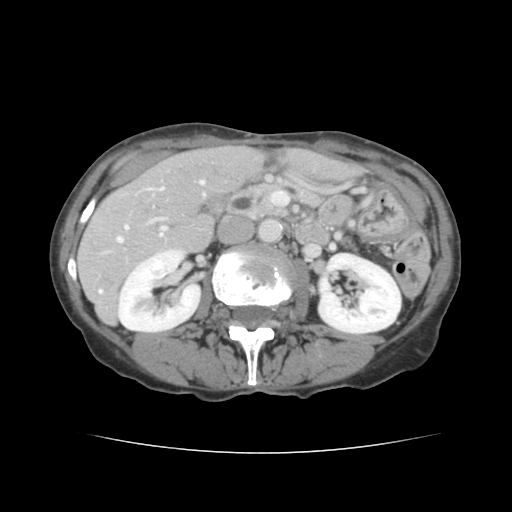
Contrast-enhanced abdominal CT, one axial slice. Position 61 of 136 along the scan axis. 120 kVp. Intravenous contrast given. Soft-tissue window (W 400 / L 40 HU). 512 × 512 image matrix, field of view 319 × 319 mm. Female patient, age 77 years. From the clinical record (not read from this slice): diagnosis: colorectal cancer liver metastases, imaged before liver resection; multiple liver metastases: yes; largest metastasis: 3 cm; disease in both lobes: no.
Structures marked on this image (manually delineated by an expert):
- hepatic veins: box from (x=118, y=181) to (x=204, y=242) px
- liver: (x=79, y=146)–(x=266, y=322)
- planned liver remnant (the part of the liver to remain after resection): (x=164, y=146)–(x=264, y=203)
- portal vein (with intrahepatic branches): (x=99, y=221)–(x=166, y=293)